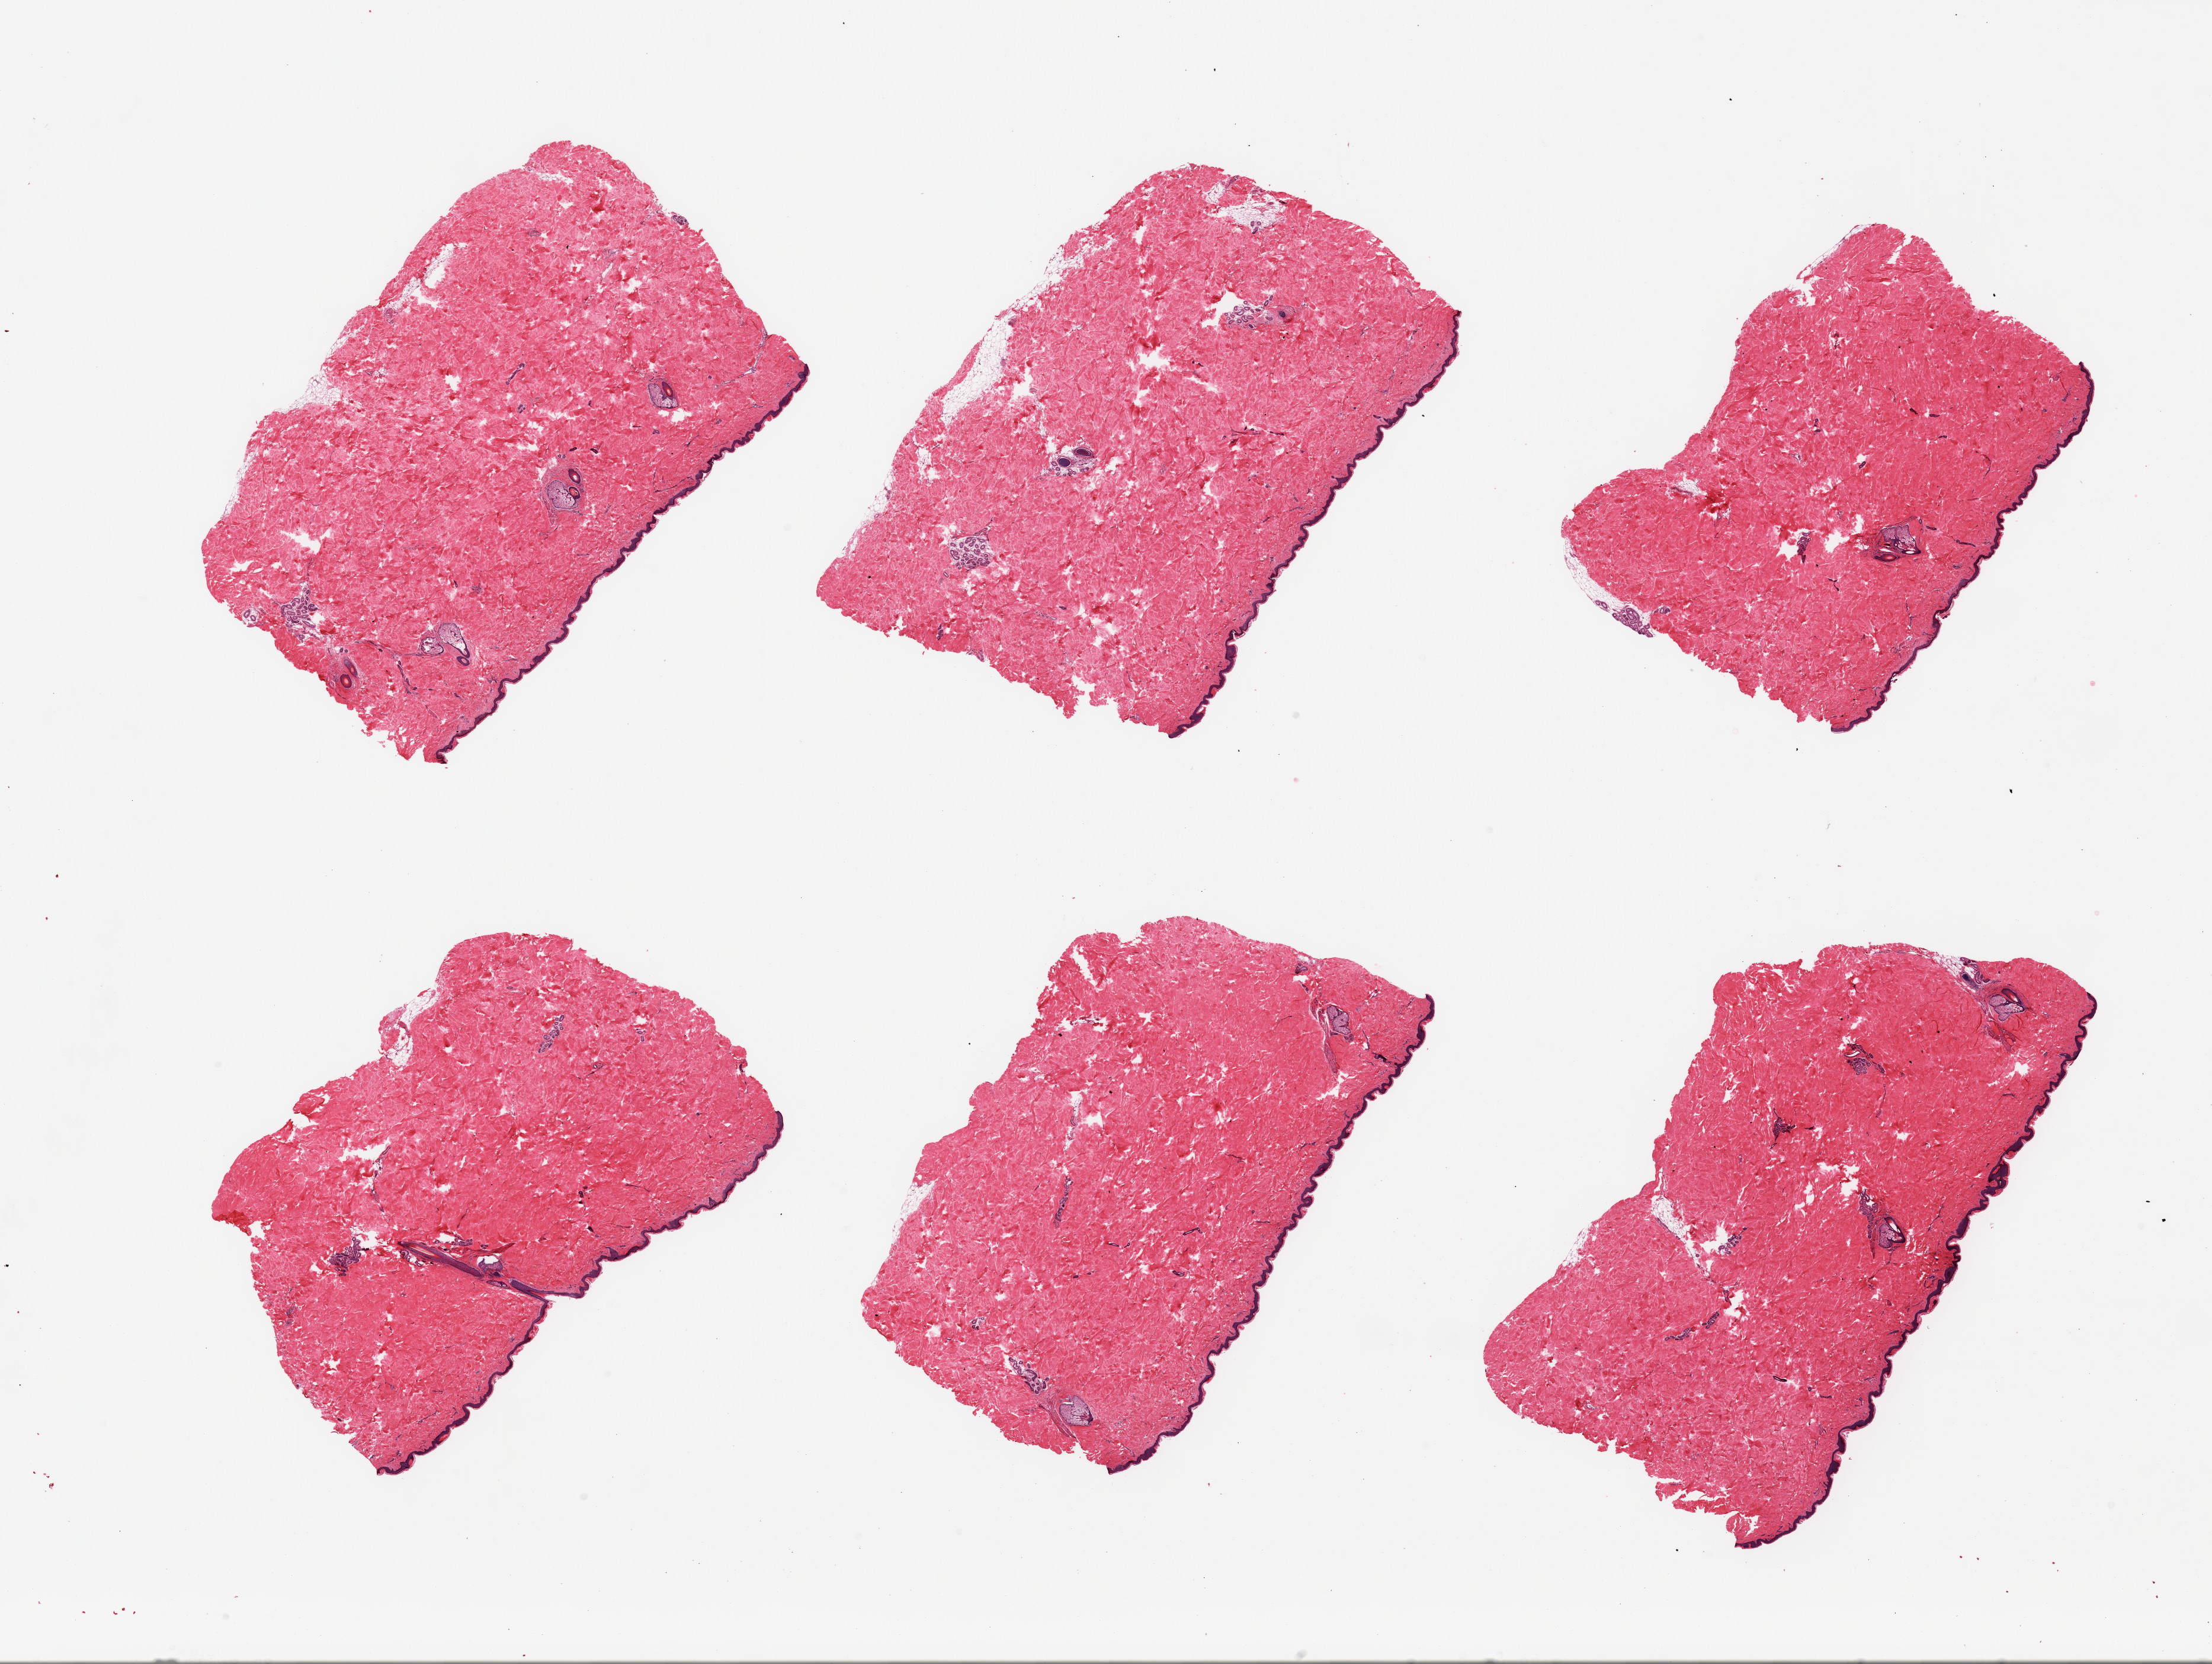
Hematoxylin and eosin (H&E) whole-slide image — whole scanned area (about 29.5 x 22.2 mm, acquisition: 20x scan) shown as a low-resolution overview, PAXgene-fixed, paraffin-embedded tissue, sampled site (target tissue): skin of suprapubic region, donor tissue sample. Donor: male.
• reviewer comment on this tissue sample: 6 pieces; several hair follicles; well trimmed; 1% dermal fat